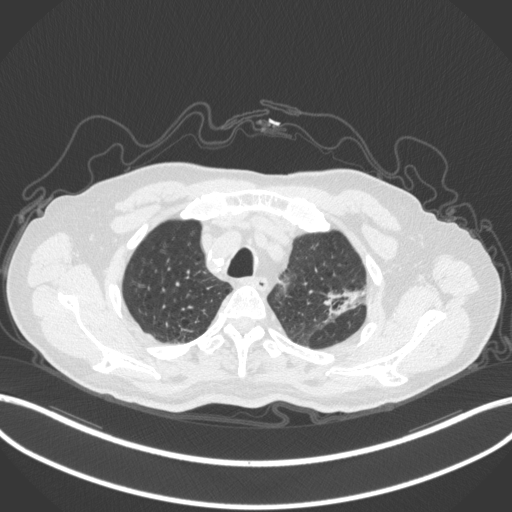
Chest CT, one axial slice; position 251 of 331 along the scan axis; reconstruction kernel B31f; lung window (W 1500 / L -600 HU); 1 mm slice thickness; 512 × 512 image matrix, field of view 400 × 400 mm. Male patient, age 79 years. From the clinical record (not read from this slice): clinical TNM (as recorded): T2a N1 M1; histopathological grade: G3.
Outlined on this slice (rectangle marked by the reading radiologist):
- lung tumour (recorded histology: adenocarcinoma): box from (x=317, y=284) to (x=373, y=321) px